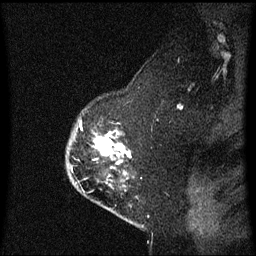
Breast MRI (dynamic contrast-enhanced), one sagittal slice; slice 46 of 60 in the series (ordered by position); dynamic contrast-enhanced series, image 2 of 3 at this slice position (ordered by acquisition); 1.5 T; TE 4.2 ms, TR 8.4 ms; 2 mm slice thickness; 256 × 256 image matrix. Patient: female, 54 years. From the clinical record (not read from this slice): setting: breast cancer imaged before/during neoadjuvant chemotherapy; receptor status: HER2-positive.
Structures marked on this image (semi-automatic segmentation, software-assisted and operator-edited):
- analysis volume of interest (the breast-tissue region the enhancement analysis was run in; not a lesion): bounding box <69,120,133,193> (left, top, right, bottom; pixels)
- tumour enhancement mask (voxels above the 70 % enhancement threshold inside the analysis volume of interest): <97,137,124,156>